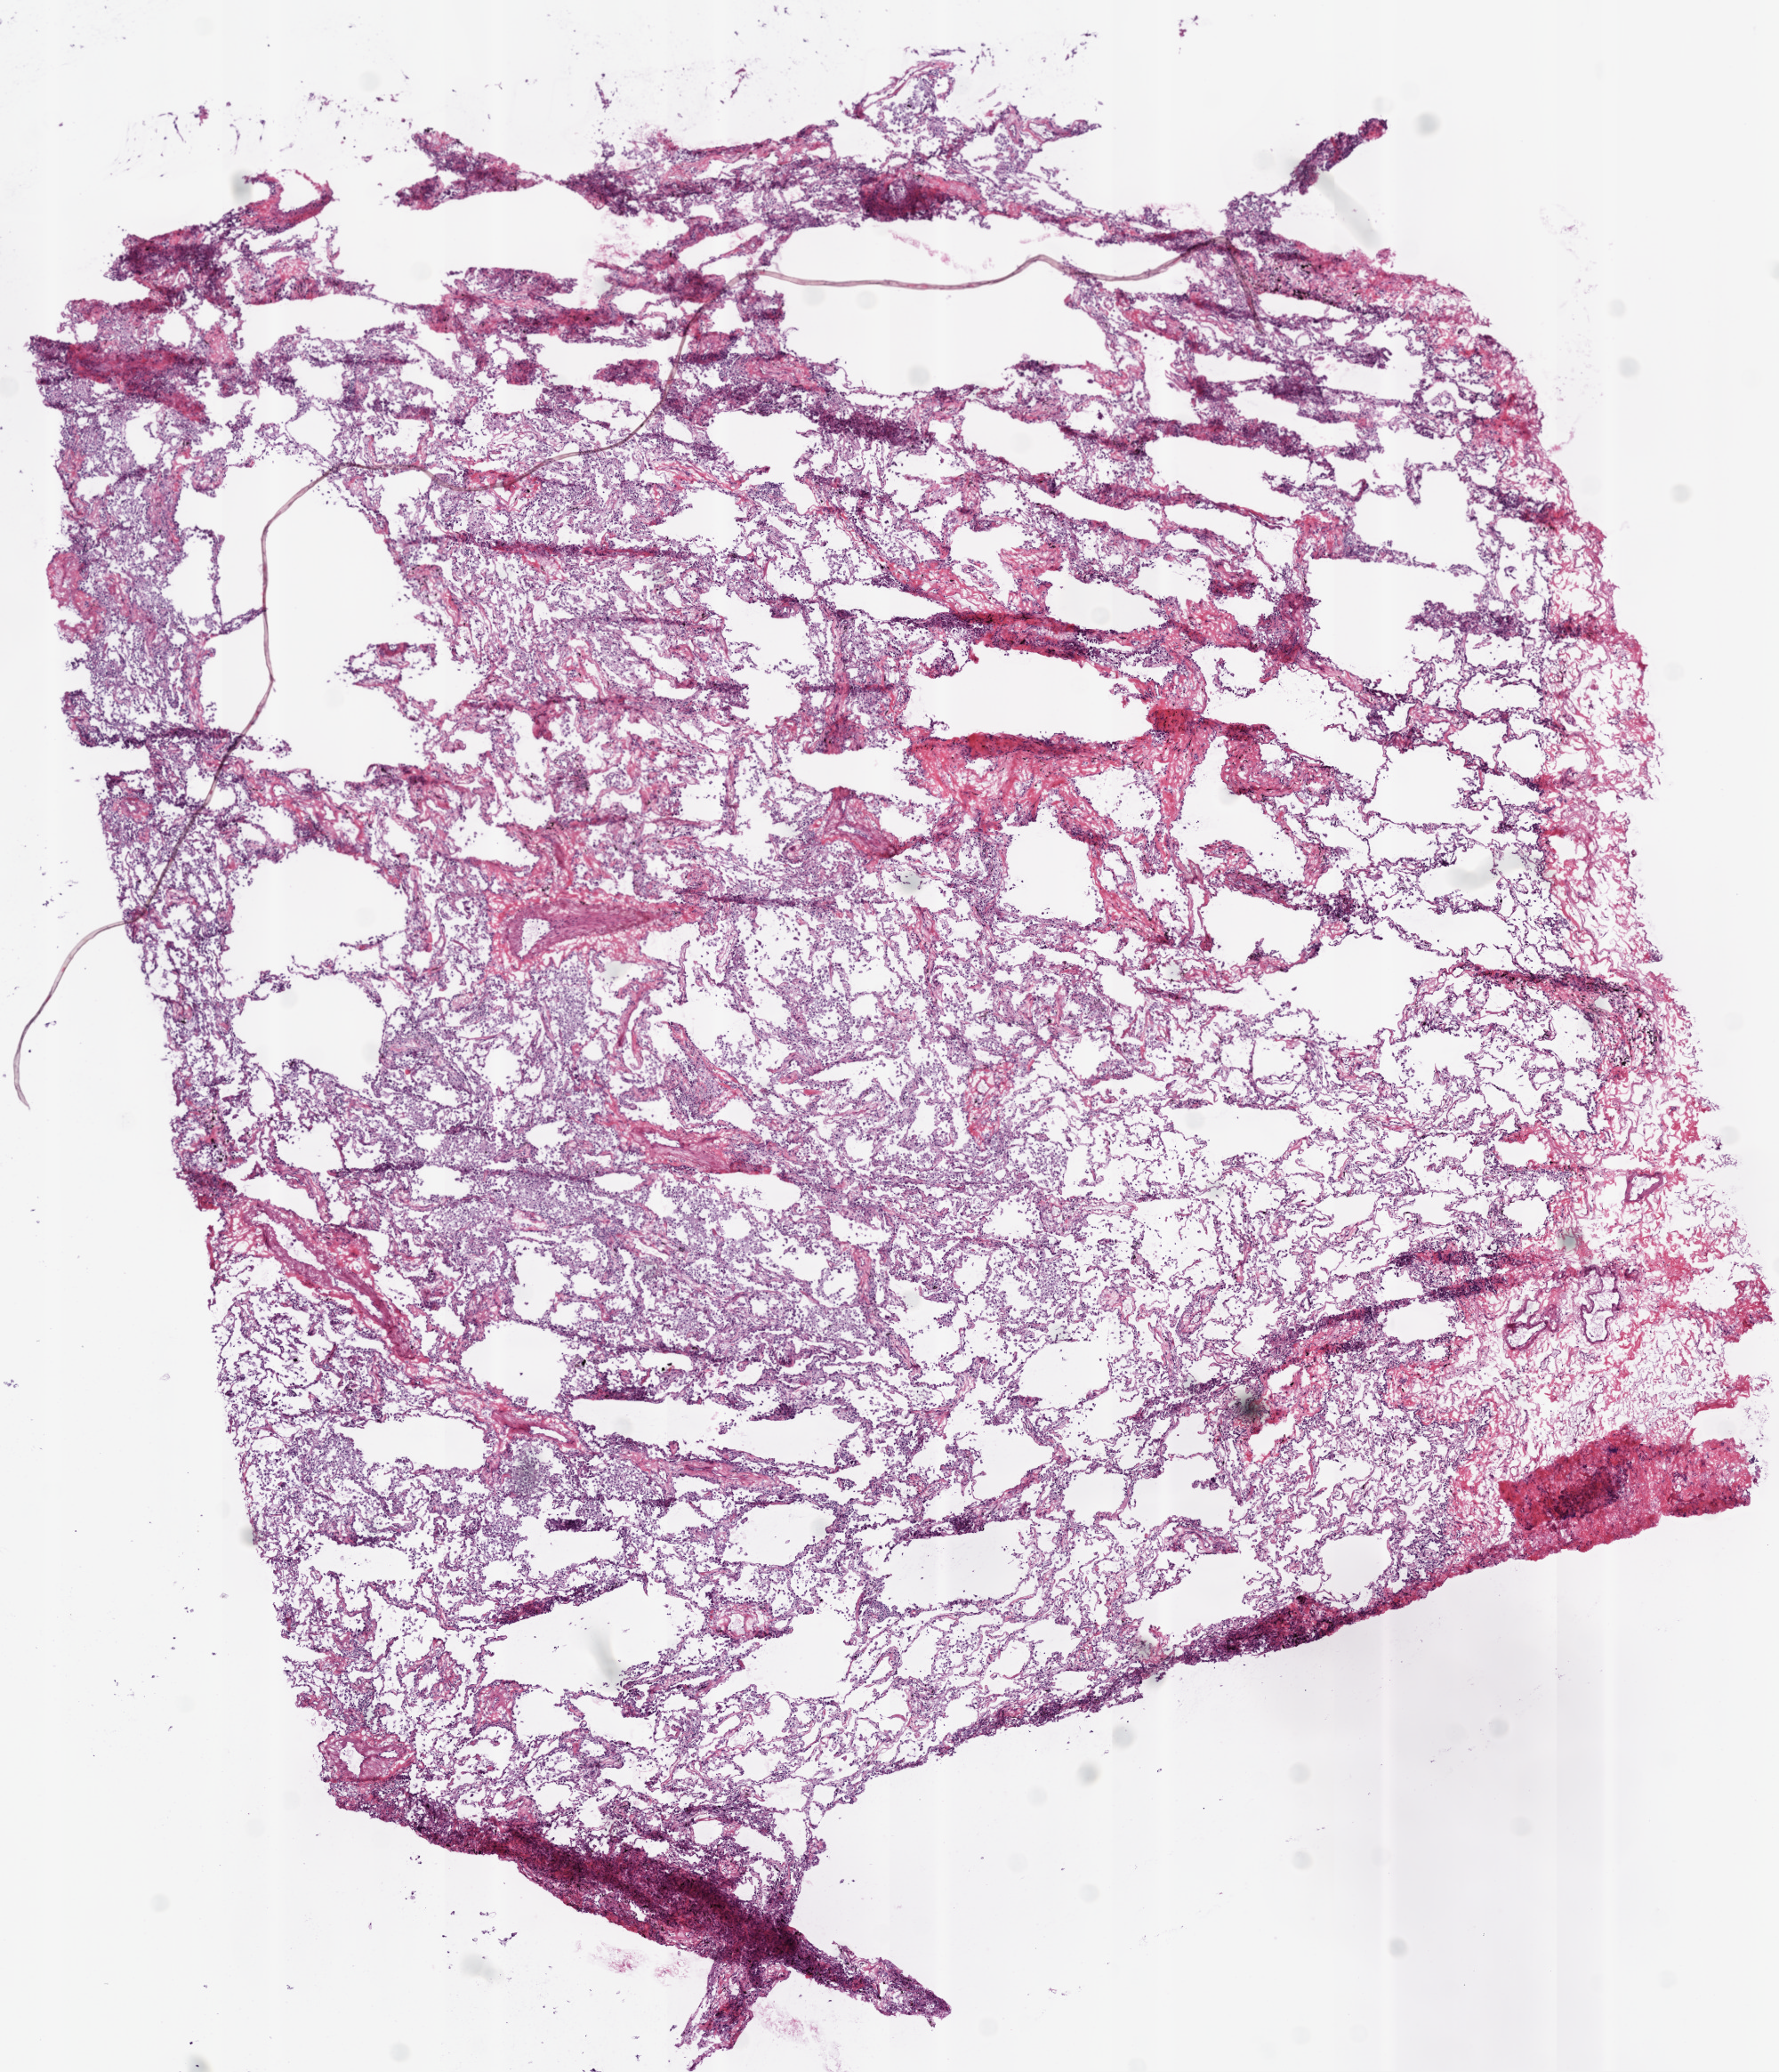
Digitized H&E tissue section (whole slide) — whole scanned area (about 8.0 x 9.3 mm) shown as a low-resolution overview, frozen section, solid tissue normal (non-tumour tissue) sample from the lung. Male, age 68 years at initial diagnosis.
This section: solid tissue normal sample (biorepository sample class). Patient diagnosis: Squamous cell carcinoma, NOS.